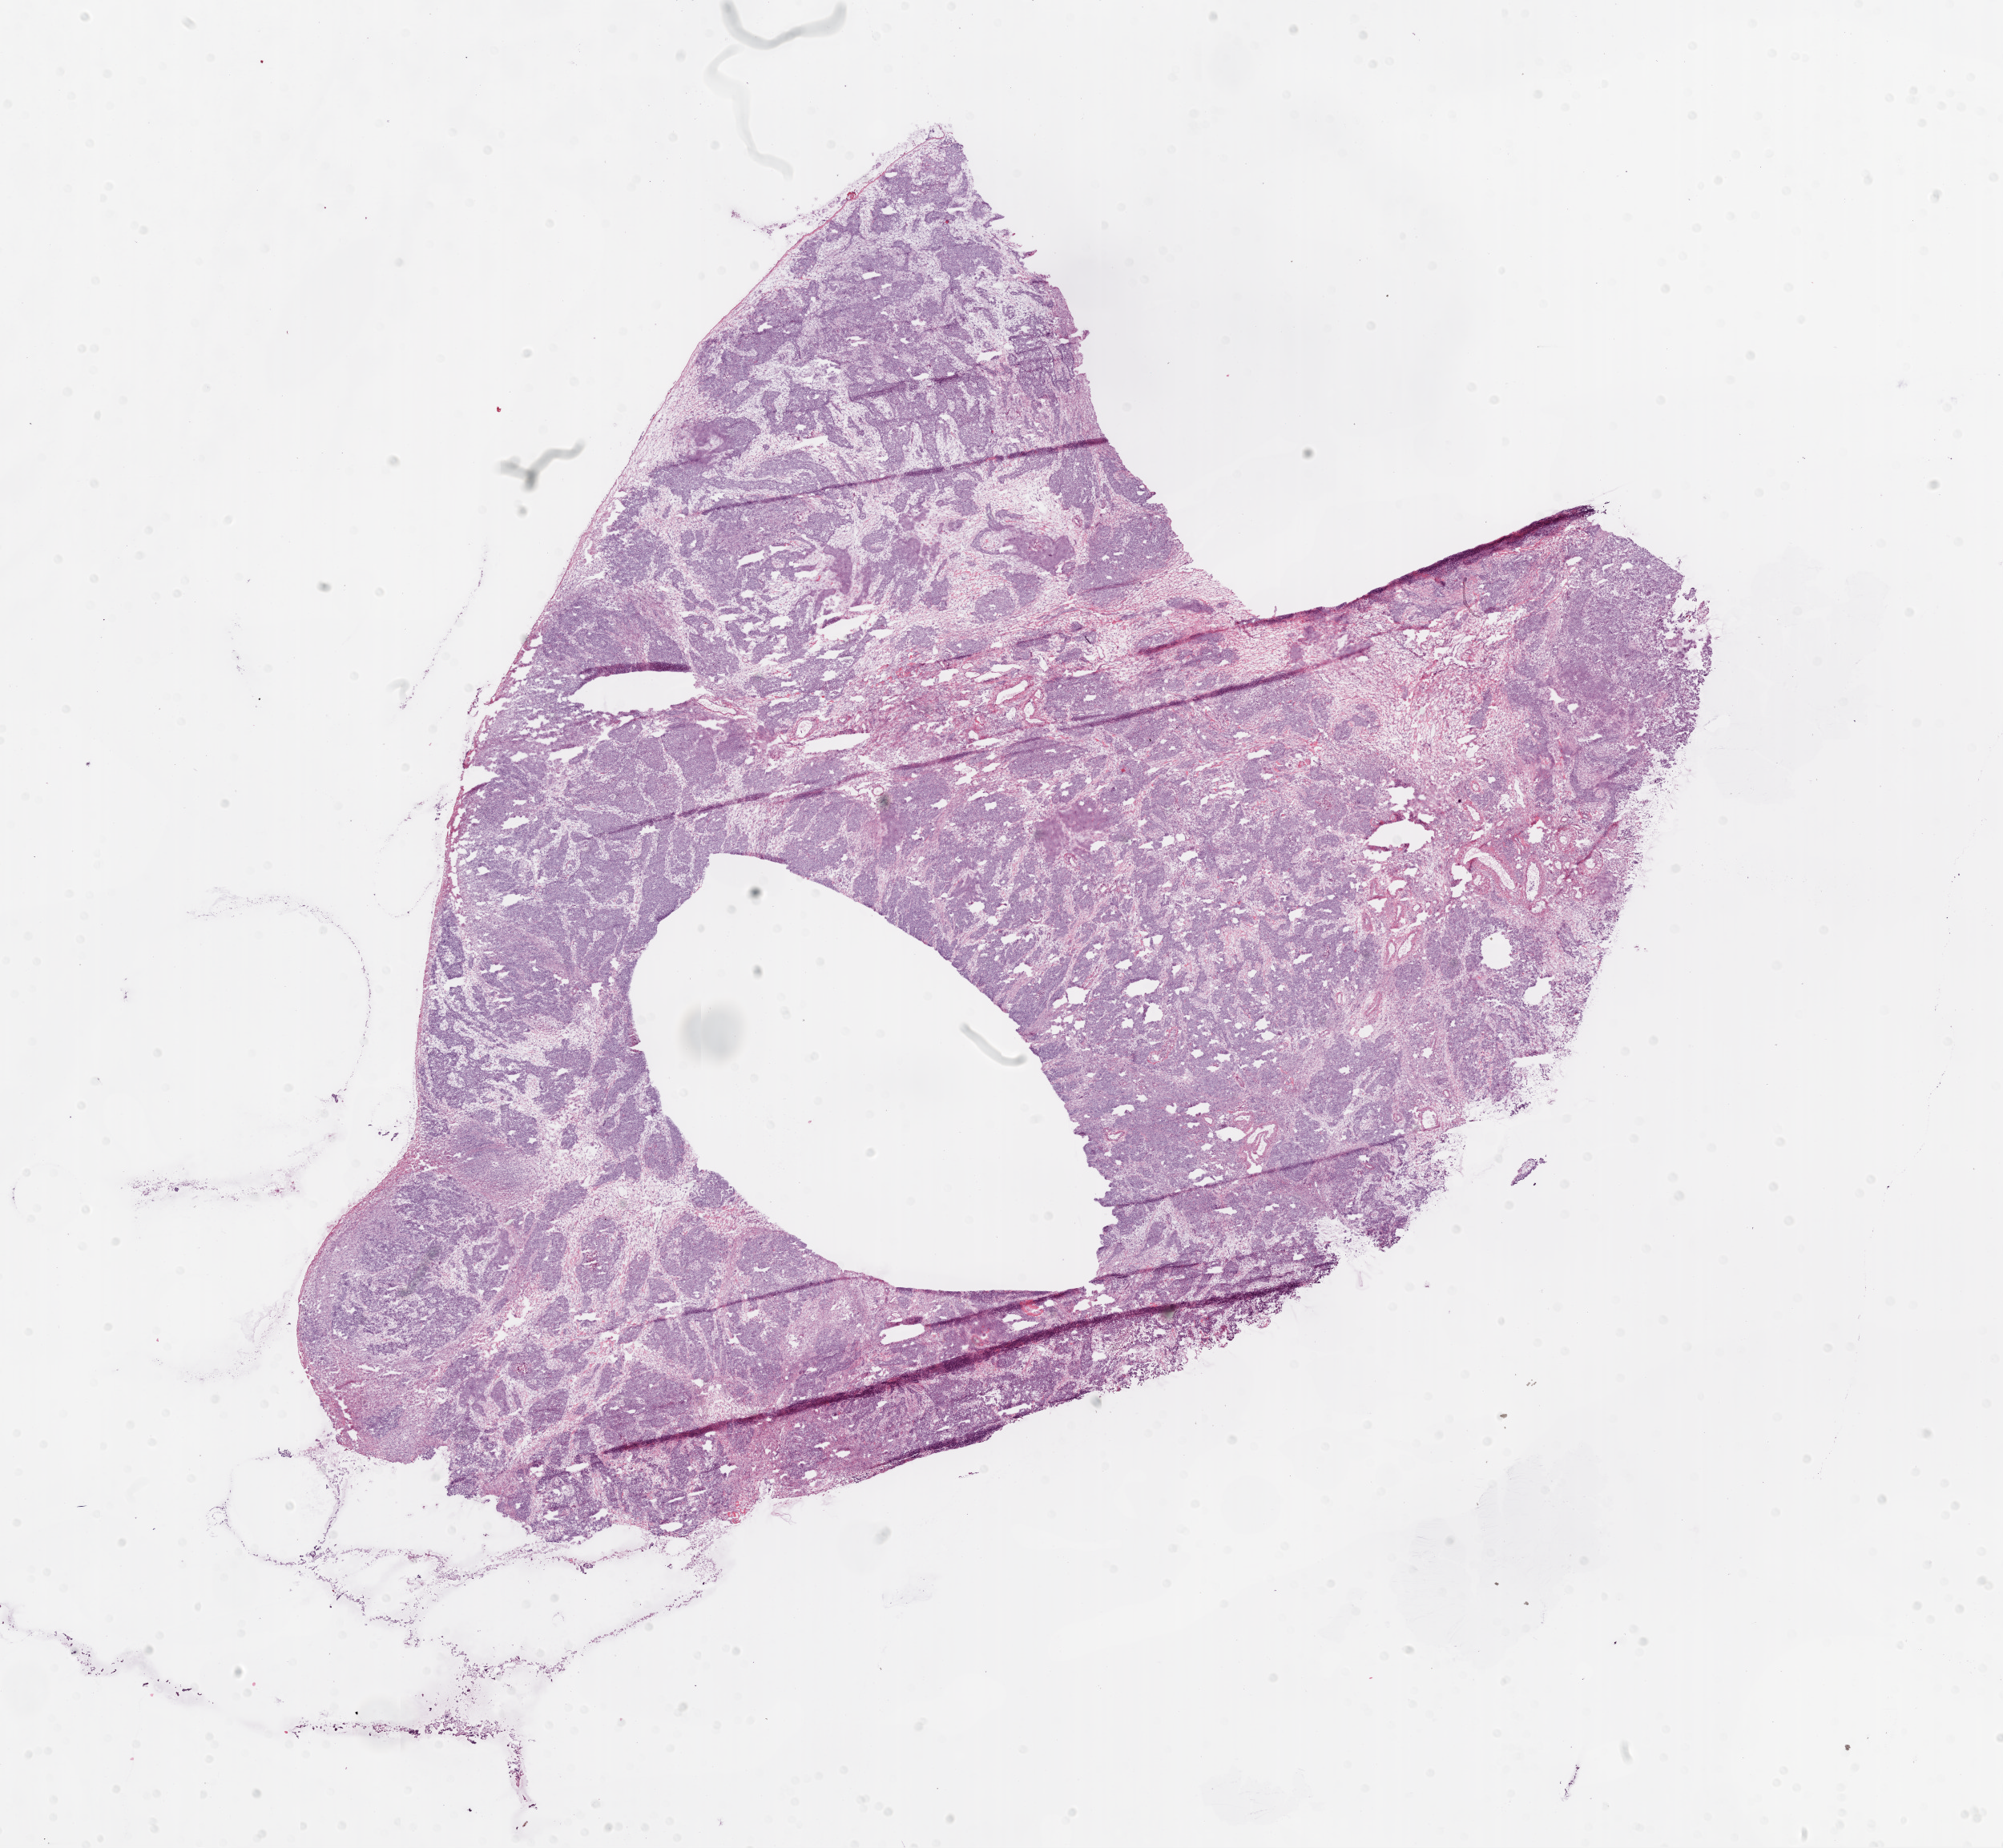
Hematoxylin and eosin (H&E) stained whole-slide image — shown as a low-resolution overview of the whole scanned area (about 20.1 x 18.5 mm). Frozen section. Sample: primary tumour, ovary. Female, age 53 years at initial diagnosis. Histologic grade: G2 (moderately differentiated). Pathologist review of this section (percent, as recorded): tumour cells 85%, tumour nuclei 95%, normal cells 7%, stromal cells 5%, necrosis 3%.
- FIGO stage: IIIC
- laterality: bilateral
- diagnosis: Serous cystadenocarcinoma, NOS